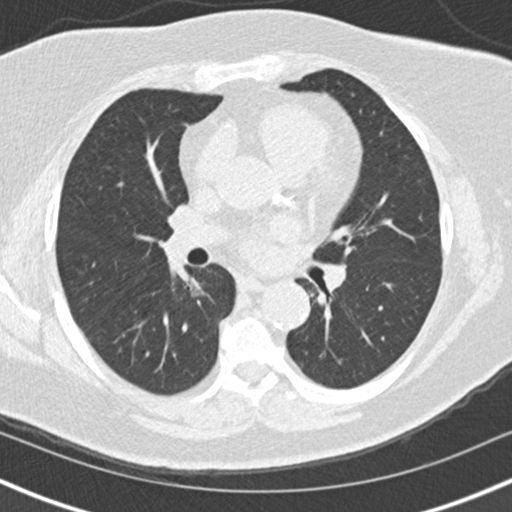
Low-dose screening chest CT, one axial slice; position 86 of 152 along the scan axis; 120 kVp; lung window (W 1500 / L -600 HU); 2 mm slice thickness; 512 × 512 image matrix, field of view 320 × 320 mm.
Outlined on this slice (outlined manually by an expert reader):
- lesion 1 (tumor, lower lobe of right lung): bounding box (x1, y1, x2, y2) in pixels: (184, 278, 205, 296)